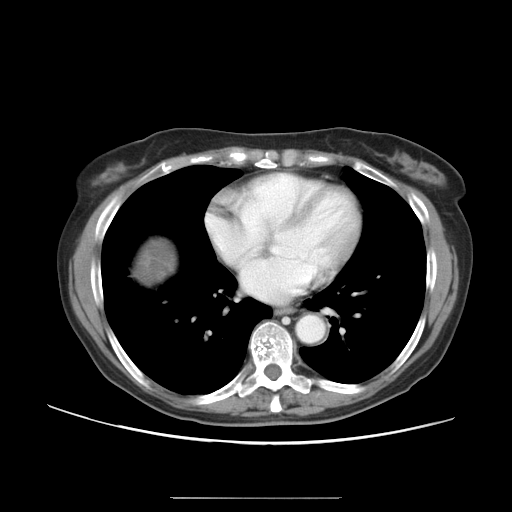
Contrast-enhanced abdominal CT, one axial slice. Position 48 of 50 along the scan axis. Soft-tissue window (W 400 / L 40 HU). 512 × 512 image matrix, field of view 389 × 389 mm. Female patient, age 58 years. From the clinical record (not read from this slice): diagnosis: colorectal cancer liver metastases, imaged before liver resection; multiple liver metastases: yes; largest metastasis: 7.3 cm; chemotherapy before resection: yes.
Structures marked on this image (manually delineated by an expert):
- liver: box from (x=135, y=240) to (x=172, y=282) px
- liver metastasis: (x=139, y=245)–(x=170, y=279)